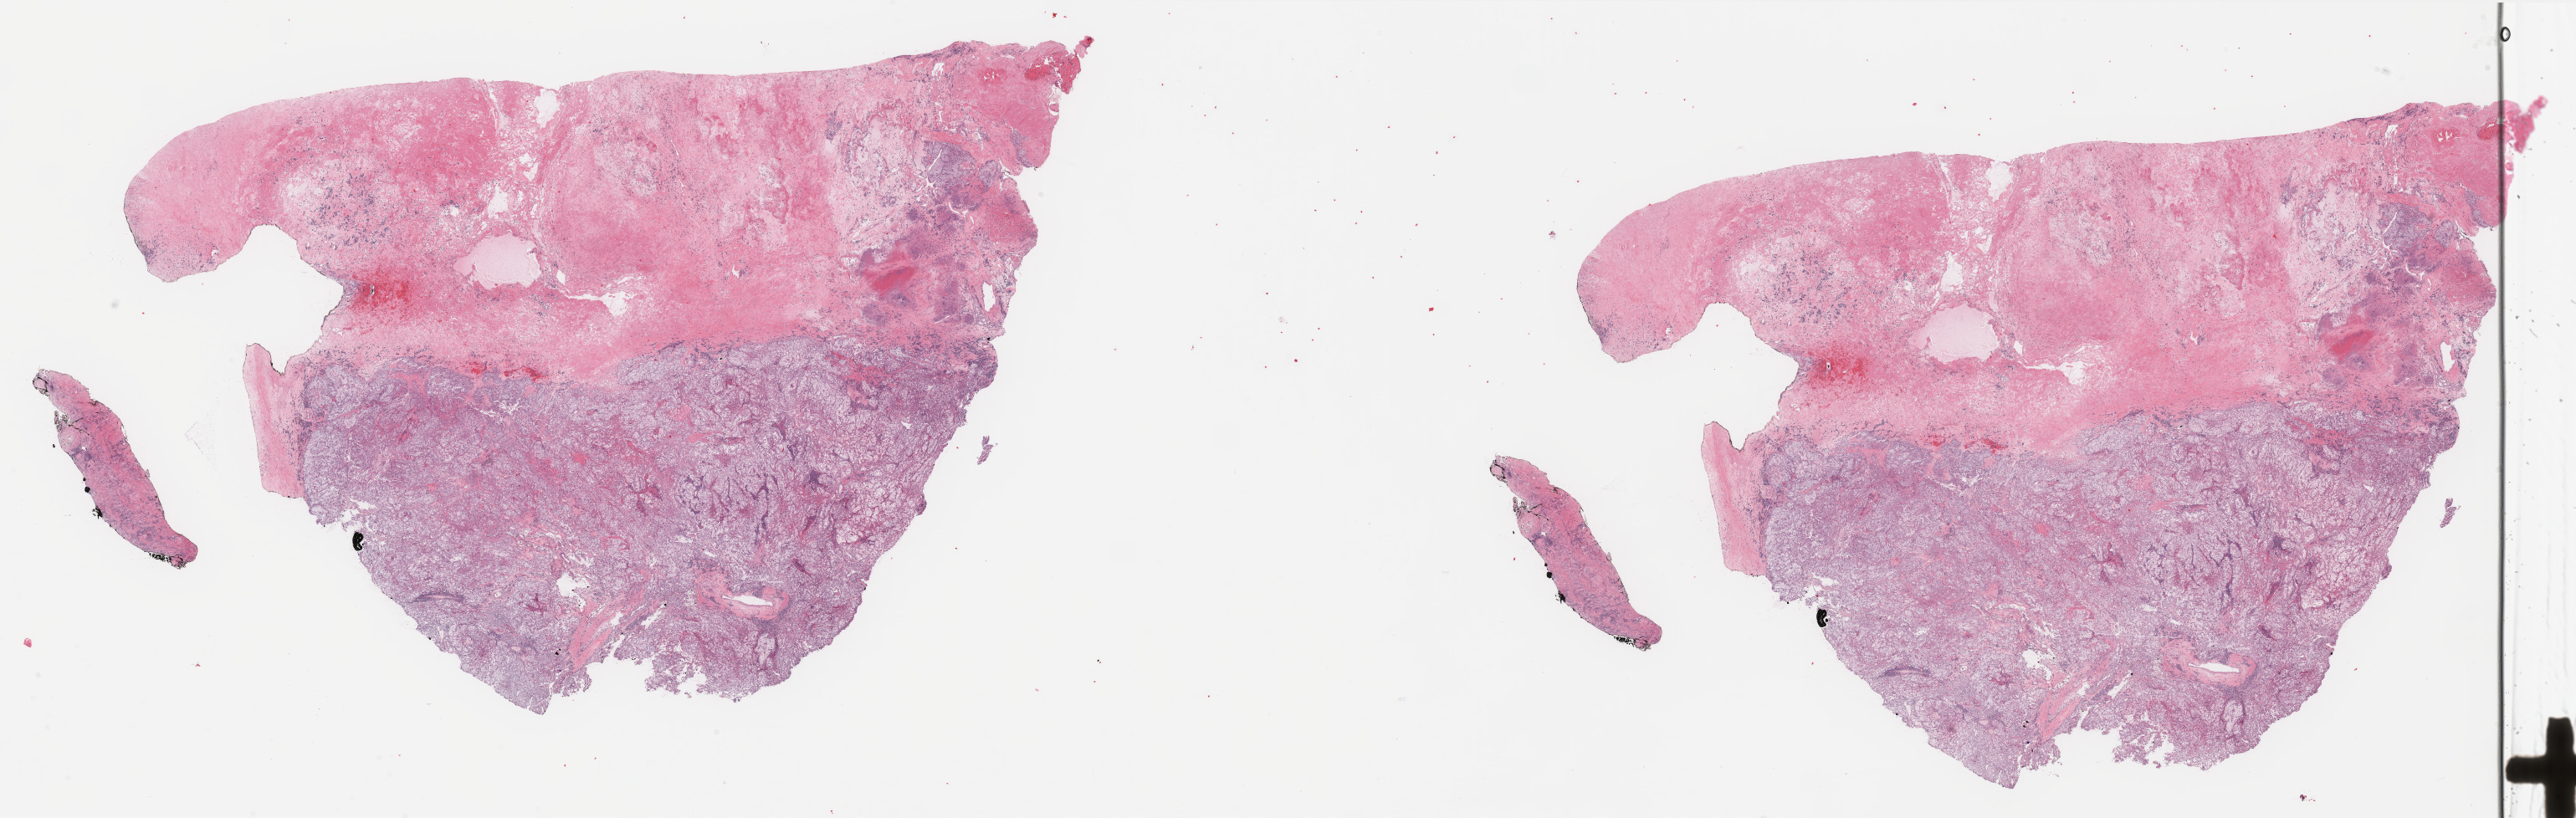
Digitized H&E tissue section (whole slide) — whole scanned area (about 48.7 x 15.5 mm, acquisition: 40x scan) shown as a low-resolution overview; formalin-fixed paraffin-embedded (FFPE) diagnostic section; sample: primary tumour, kidney. Male patient; age at initial diagnosis 48 years. Histologic grade: G3 (poorly differentiated).
Histologic diagnosis: Renal cell carcinoma, NOS. AJCC pathologic stage: I (7th edition).